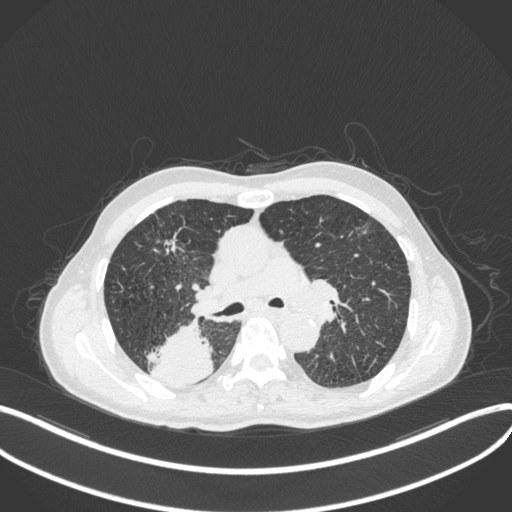
Chest CT, one axial slice. Slice 282 of 423 in the series (ordered by position). Reconstruction kernel B31f. 120 kVp. Lung window (W 1500 / L -600 HU). 512 × 512 image matrix. Male patient, age 79 years. Case-level facts recorded for this patient, not image findings: clinical TNM (as recorded): T3 N0 M0.
Annotated regions visible in this slice (bounding box drawn by a radiologist):
- lung tumour (recorded histology: adenocarcinoma): bounding box [x1, y1, x2, y2] px = [146, 327, 216, 388]